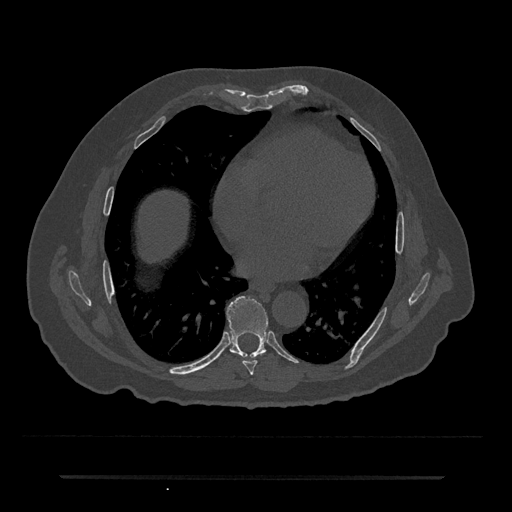
CT including the spine, one axial slice; position 357 of 797 along the scan axis; 120 kVp; bone window (W 1800 / L 400 HU); 0.5 mm slice thickness; 512 × 512 image matrix, field of view 437 × 437 mm. Male patient, age 69 years. From the clinical record (not read from this slice): primary cancer: prostate.
Outlined on this slice (semi-automatically segmented with operator editing):
- T7 vertebra: bounding box [x1, y1, x2, y2] px = [243, 353, 263, 375]
- T8 vertebra: [226, 296, 268, 358]